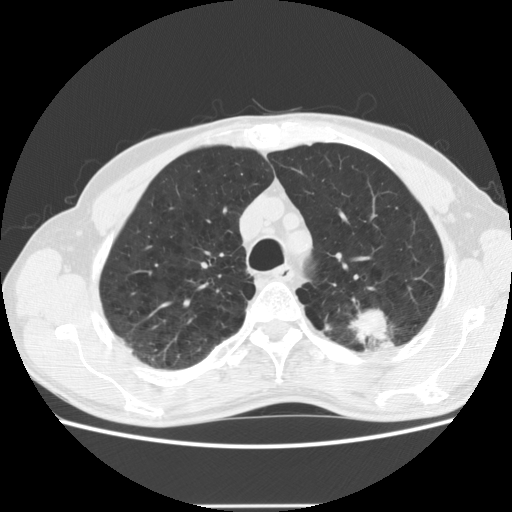
Axial slice from a low-dose chest CT screening exam; first (baseline) screen; lung window (W 1500 / L -600 HU); standard (soft-tissue) reconstruction kernel (STANDARD); 120 kVp. Male participant, aged 64 years at enrolment.
- Expert-annotated lung lesion, bounding box [x1, y1, x2, y2] px = [340, 287, 430, 359].
- Reader record for this screening exam (exam-level; its link to the box is not recorded): non-calcified nodule or mass ≥4 mm, left upper lobe, 27 × 19 mm, poorly defined margins, soft tissue attenuation.